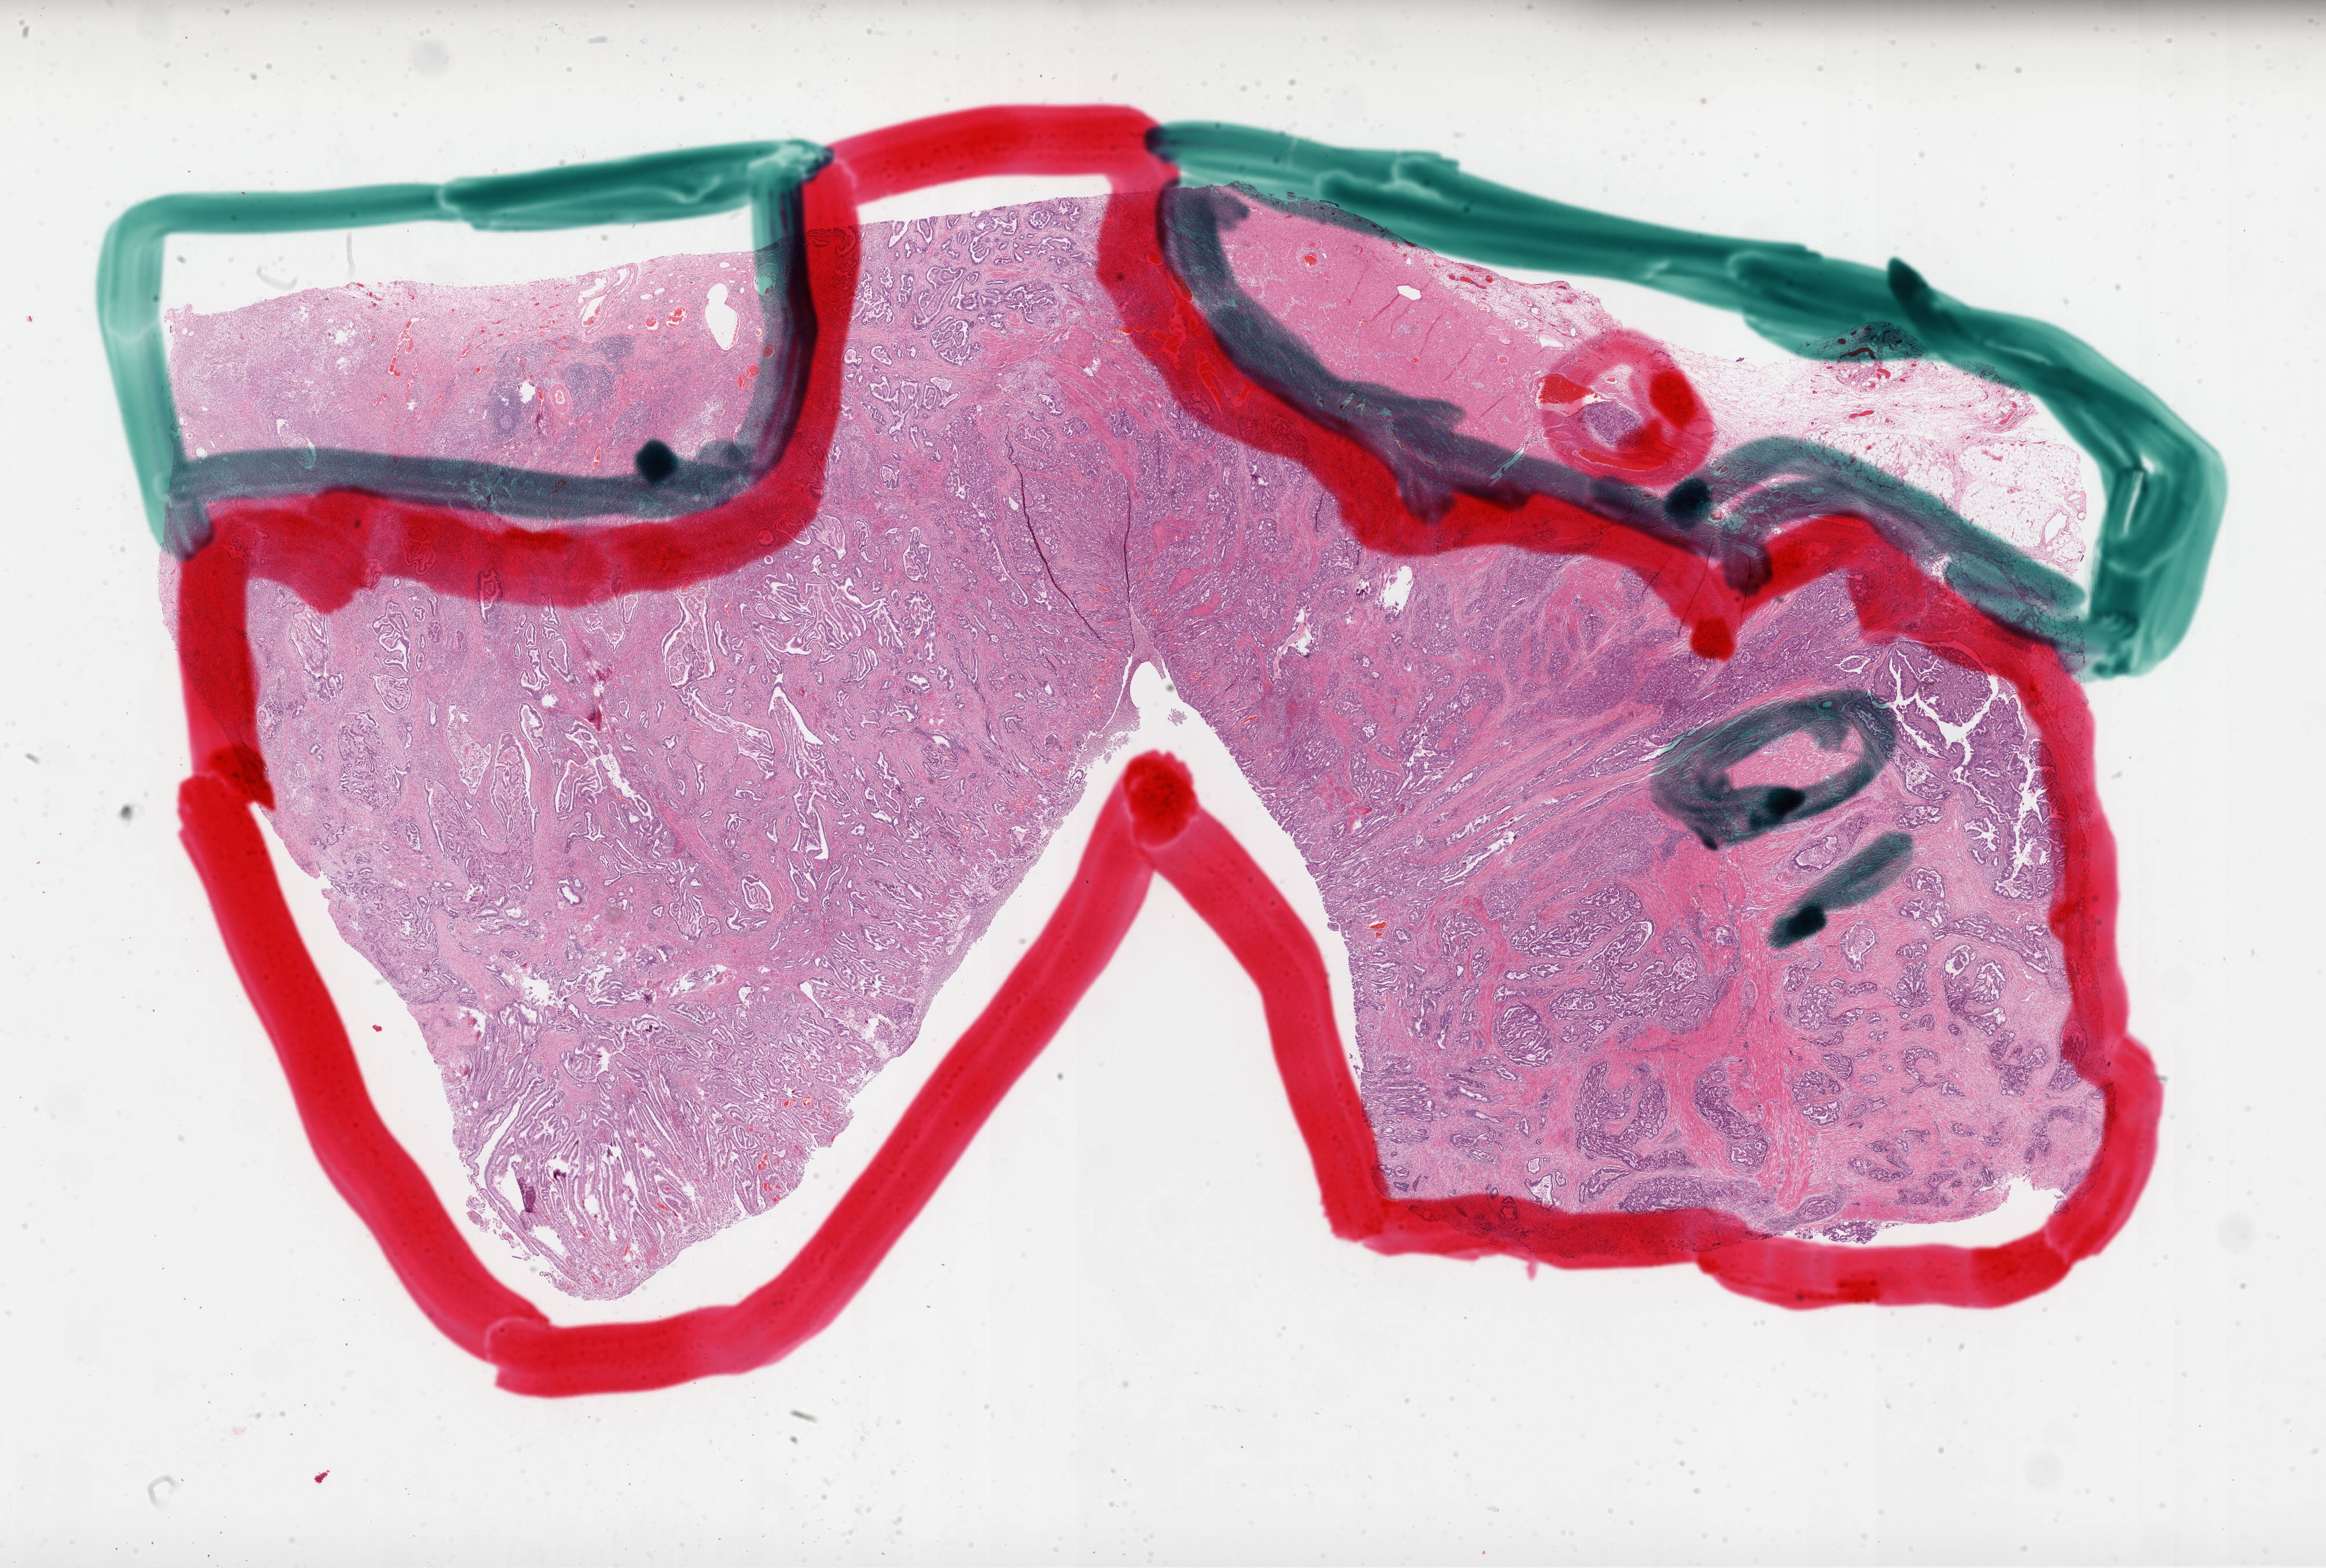
Digitized H&E-stained tissue section (whole slide), low-resolution overview of the scanned area, about 32.4 x 21.8 mm, FFPE section, sample: primary tumour, stomach. Patient: male, age at initial diagnosis 49 years. Histologic grade: G3 (poorly differentiated).
AJCC pathologic stage: II. Histologic diagnosis: Adenocarcinoma, intestinal type. Lymph nodes positive (case pathology): 0 of 5 examined.